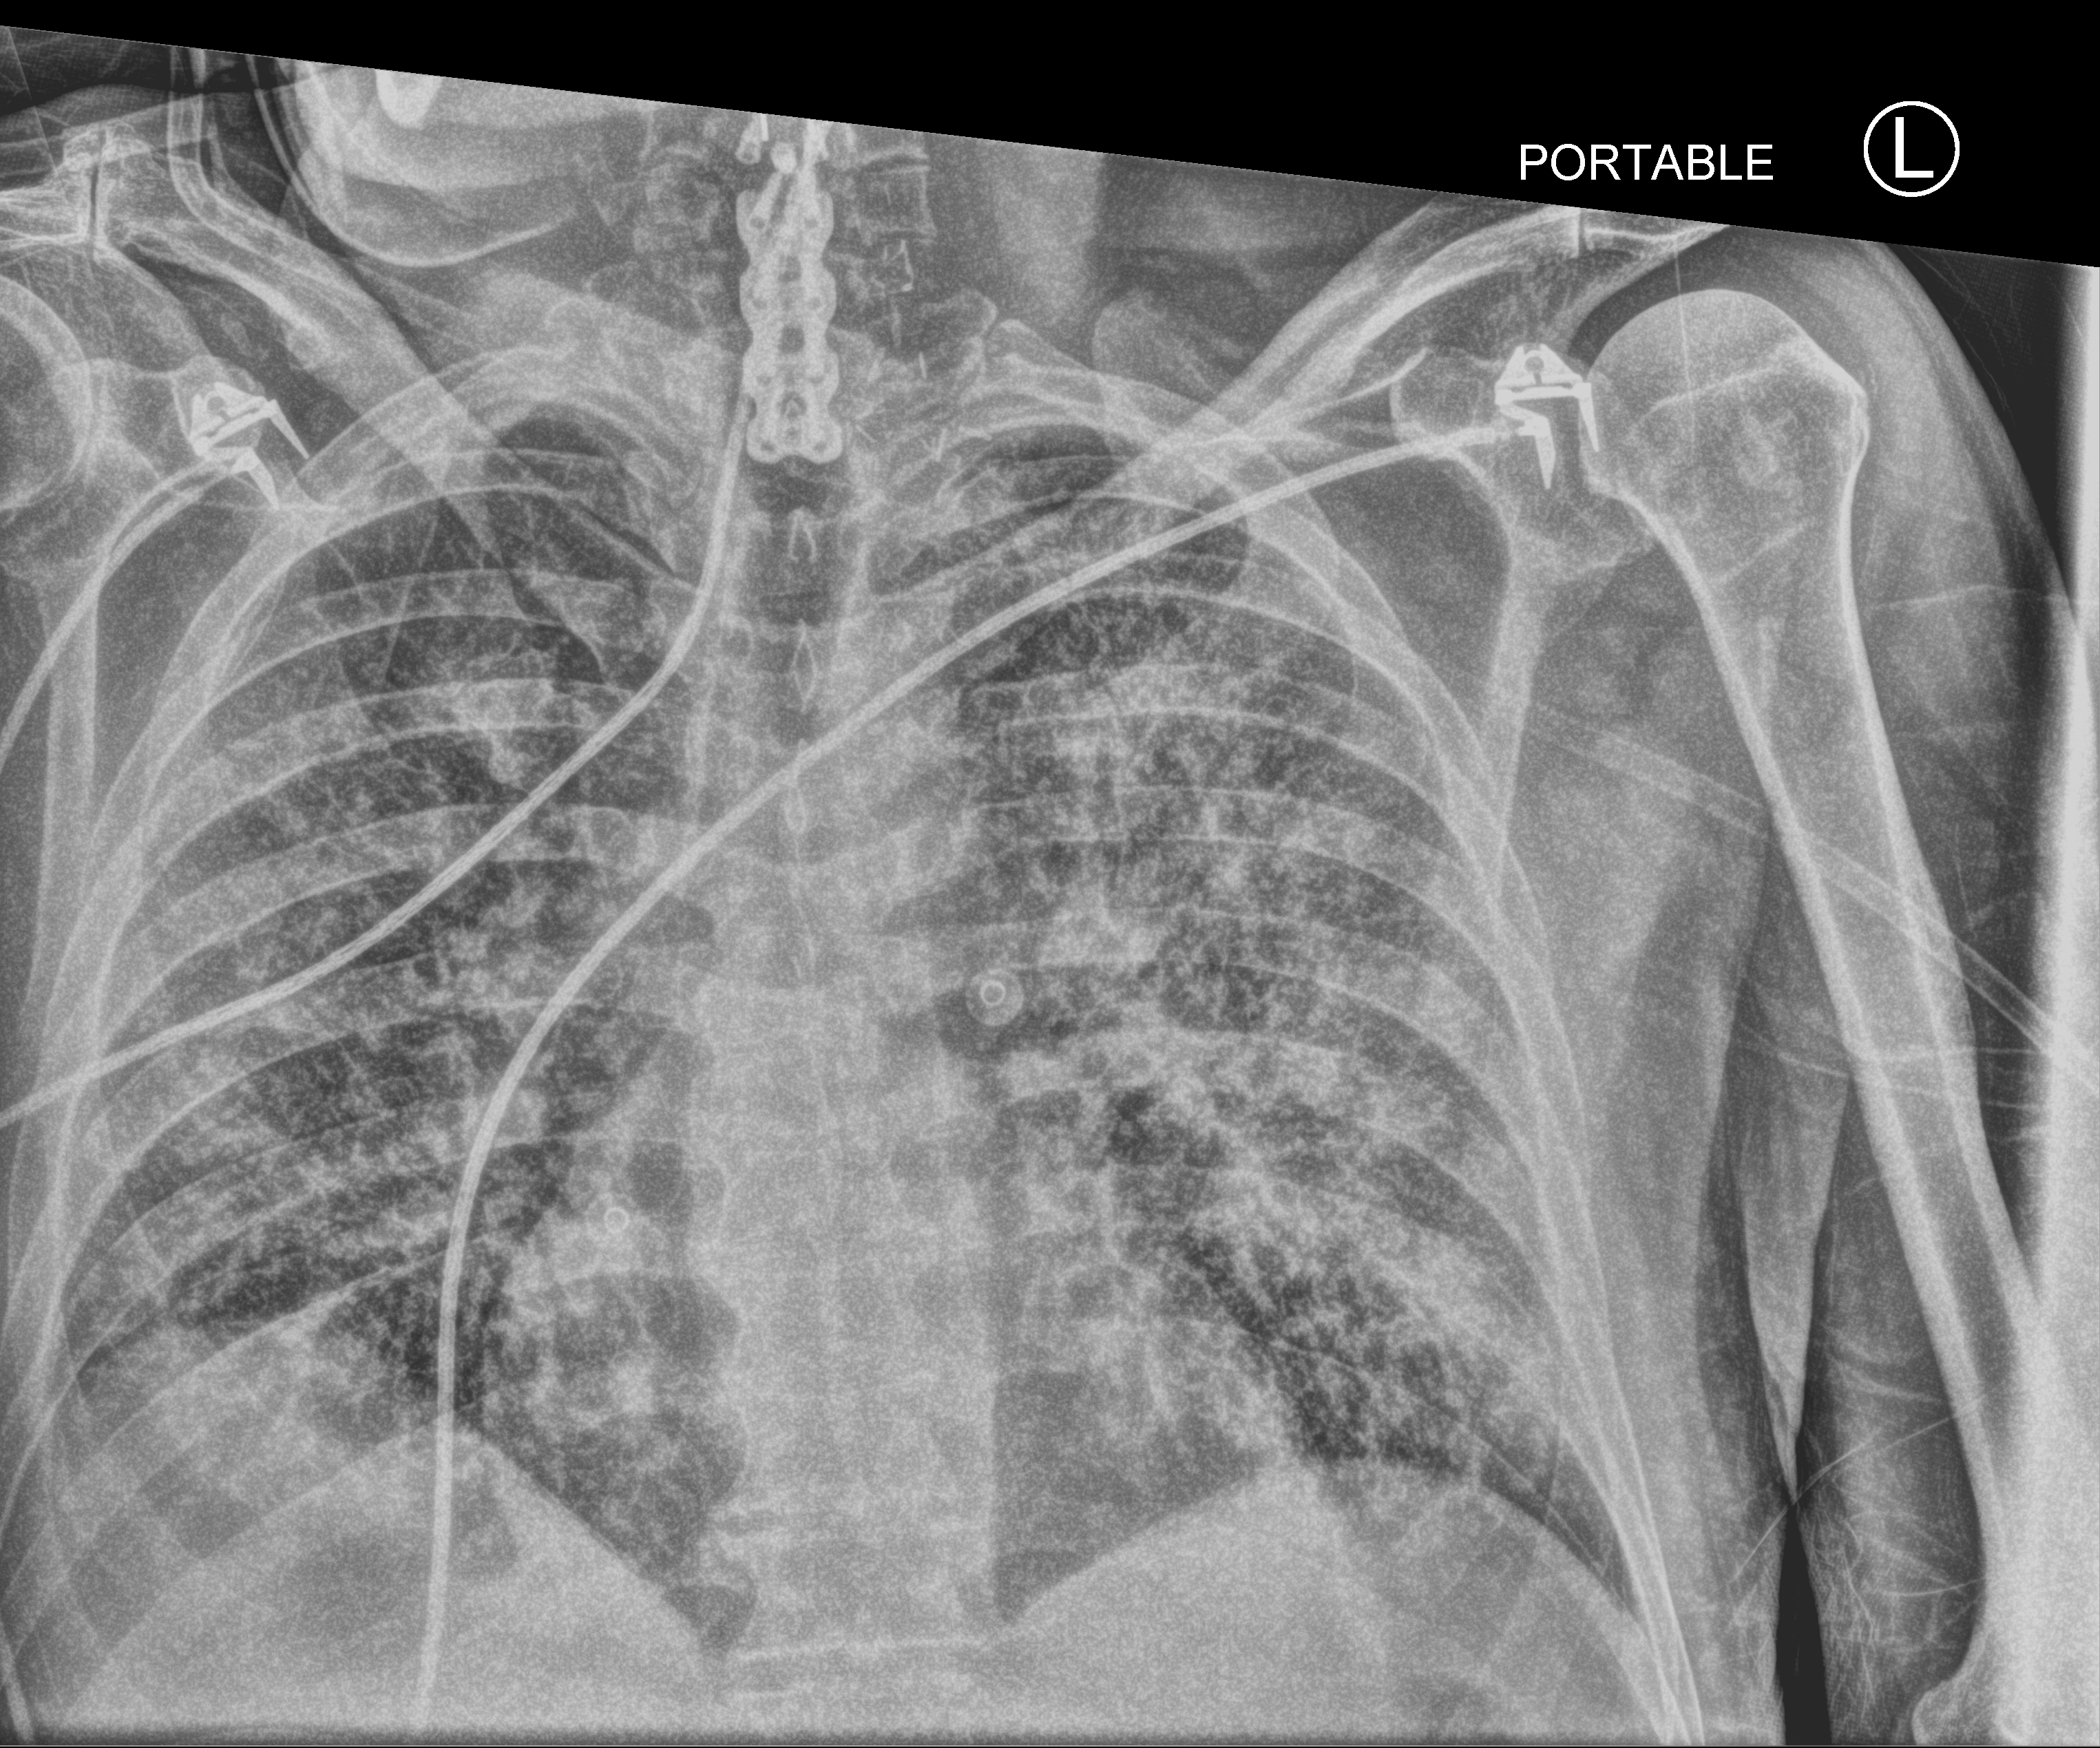
Bedside chest radiograph (computed radiography); anteroposterior (AP) projection. Patient hospitalised with COVID-19; male, aged 60–74 years.
Hospital-stay facts (about this admission, not read from this image; timing relative to this image not recorded): length of hospital stay: 43 days.